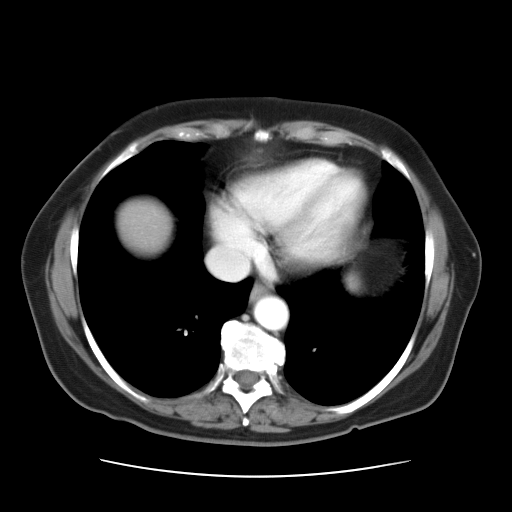
Contrast-enhanced abdominal CT, one axial slice. Slice 31 of 34 in the series (ordered by position). Reconstruction kernel STANDARD. 120 kVp. Intravenous contrast given. Soft-tissue window (W 400 / L 40 HU). 512 × 512 image matrix. Female patient, age 65 years. From the clinical record (not read from this slice): diagnosis: colorectal cancer liver metastases, imaged before liver resection; multiple liver metastases: yes; largest metastasis: 2.2 cm; disease in both lobes: no.
Outlined on this slice (expert manual segmentation):
- liver: bounding box [x1, y1, x2, y2] px = [121, 204, 166, 245]
- planned liver remnant (the part of the liver to remain after resection): [121, 204, 166, 245]